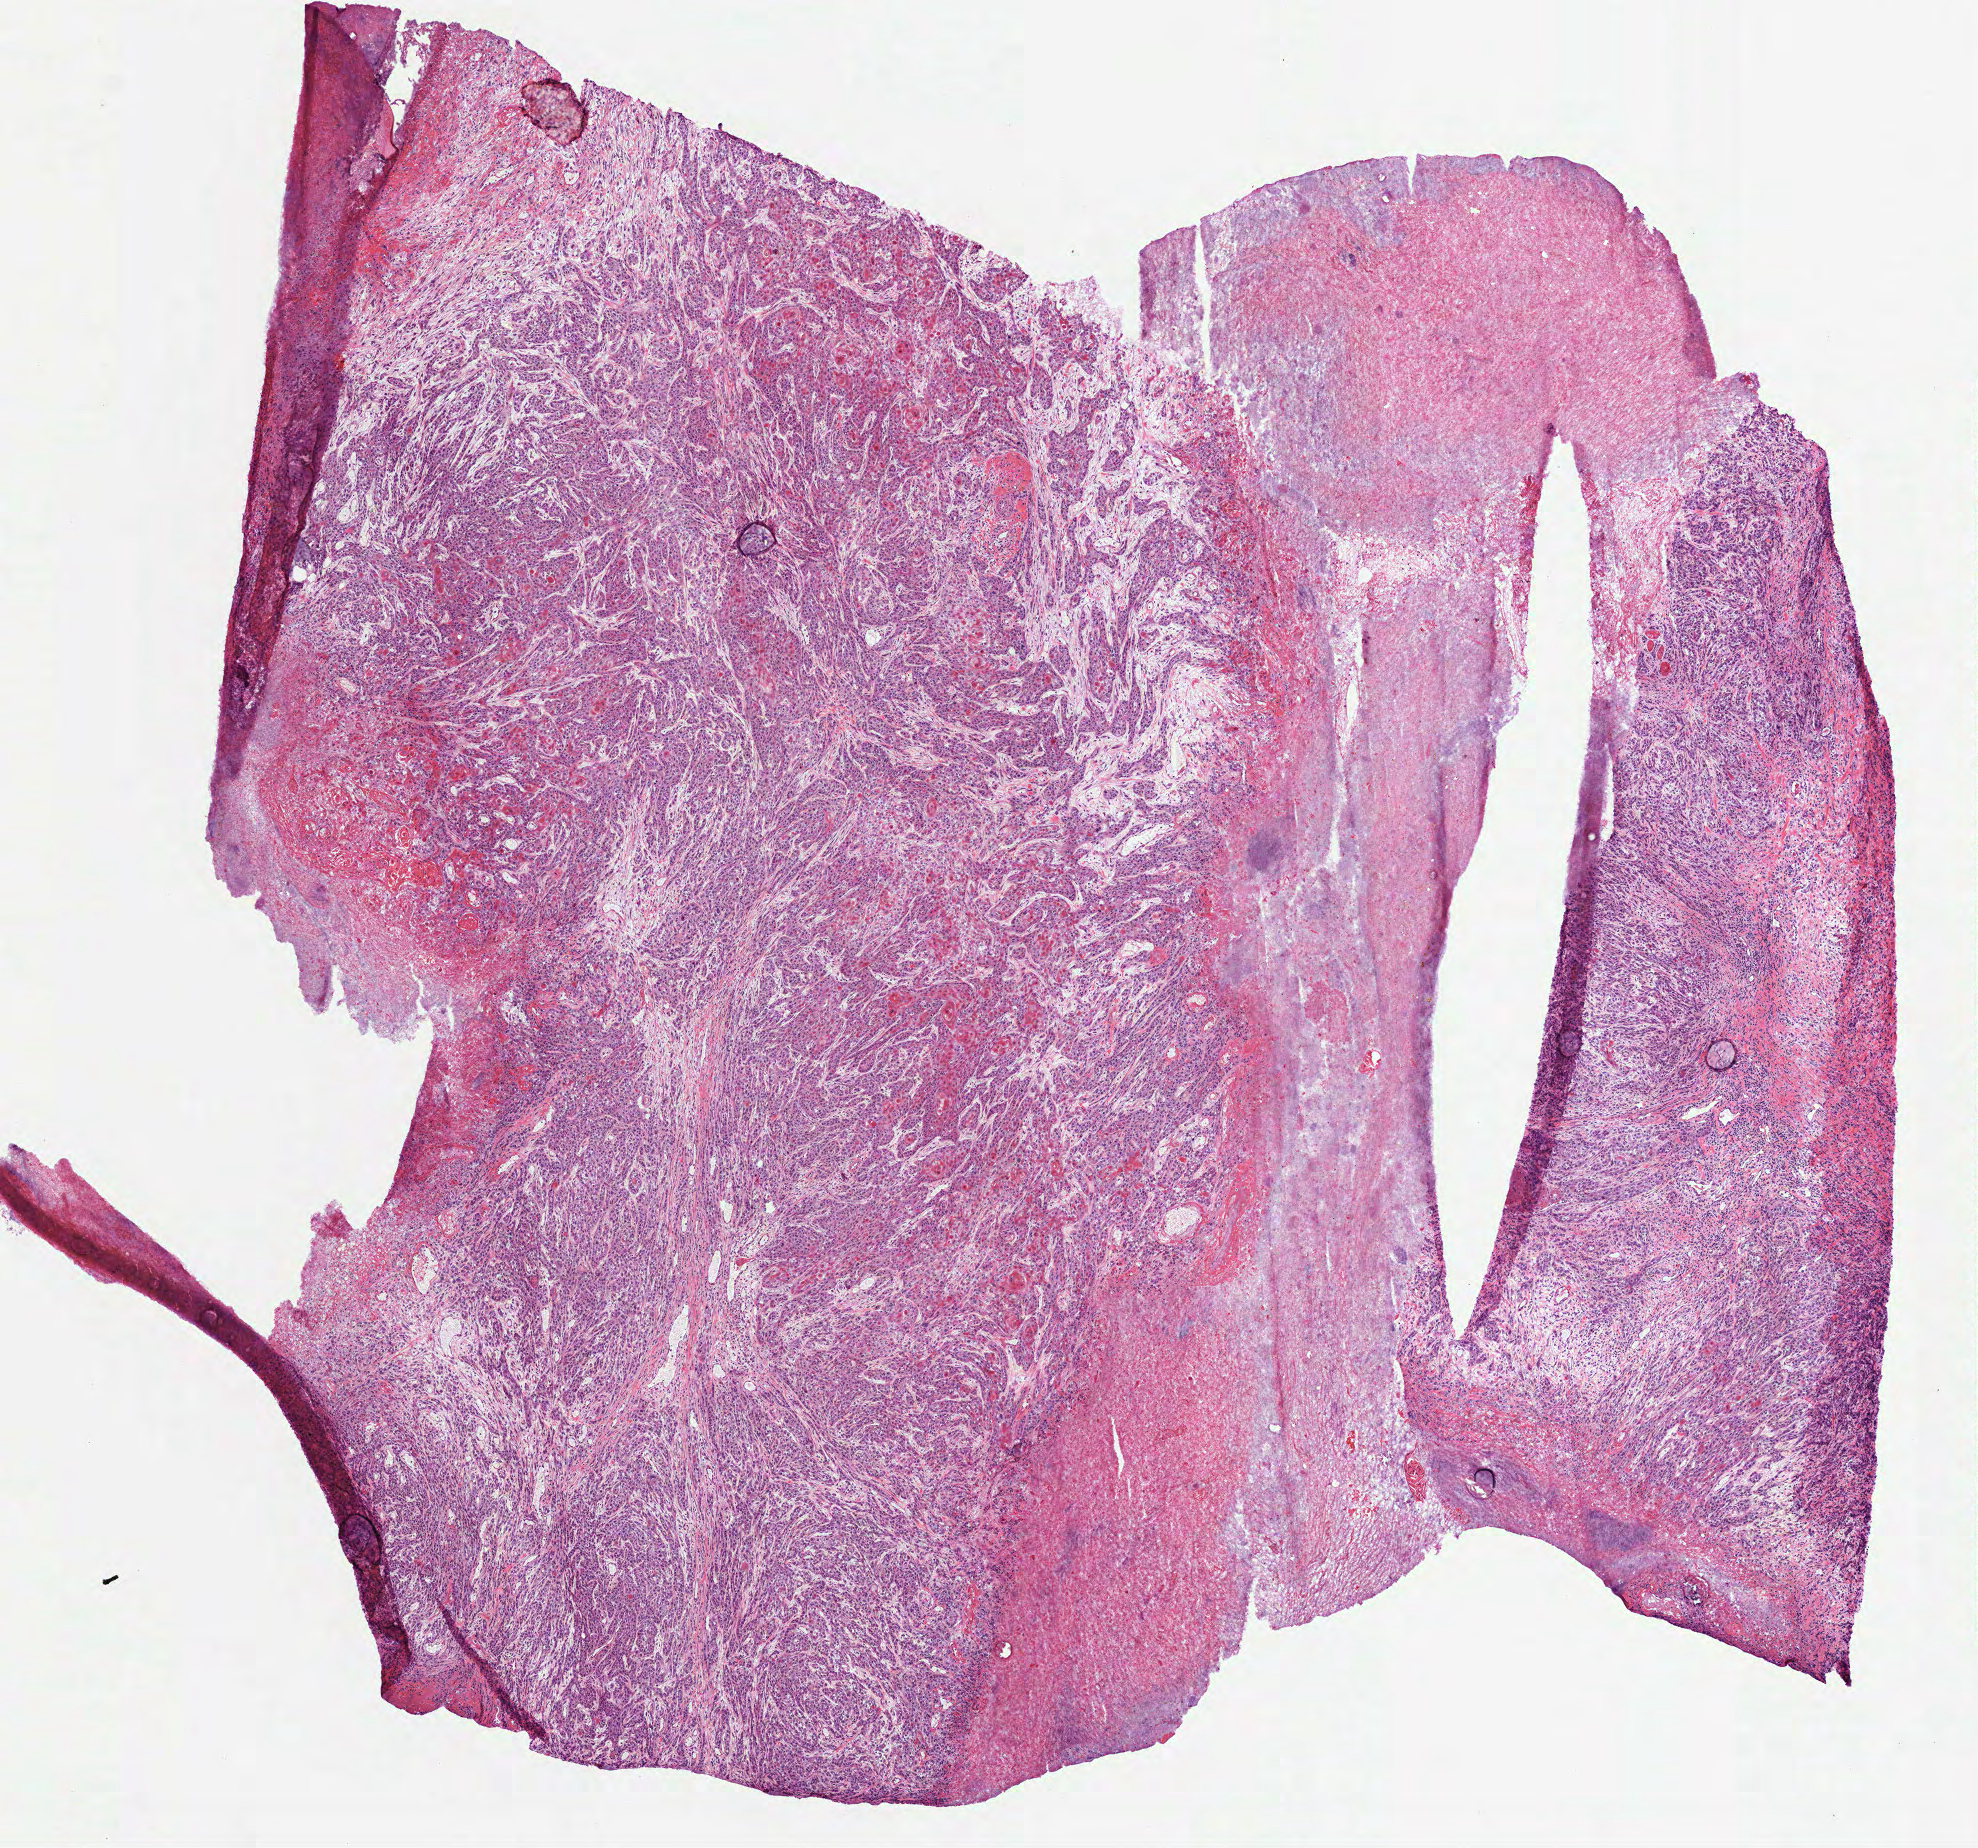
Hematoxylin and eosin (H&E) stained whole-slide image, a low-resolution overview of the entire scanned area, about 8.0 x 7.5 mm (slide scanned at 40x); frozen section from the bottom of the tissue portion; sample: primary tumour, head and neck. Patient: male, age at initial diagnosis 50 years. Histologic grade: G2 (moderately differentiated). Pathologist review of this section (percent, as recorded): tumour cells 70%, tumour nuclei 80%, normal cells 0%, stromal cells 15%, necrosis 15%.
• diagnosis: Squamous cell carcinoma, keratinizing, NOS (retromolar area)
• AJCC pathologic stage: IVA (7th edition)
• TNM: T4a N2b M0